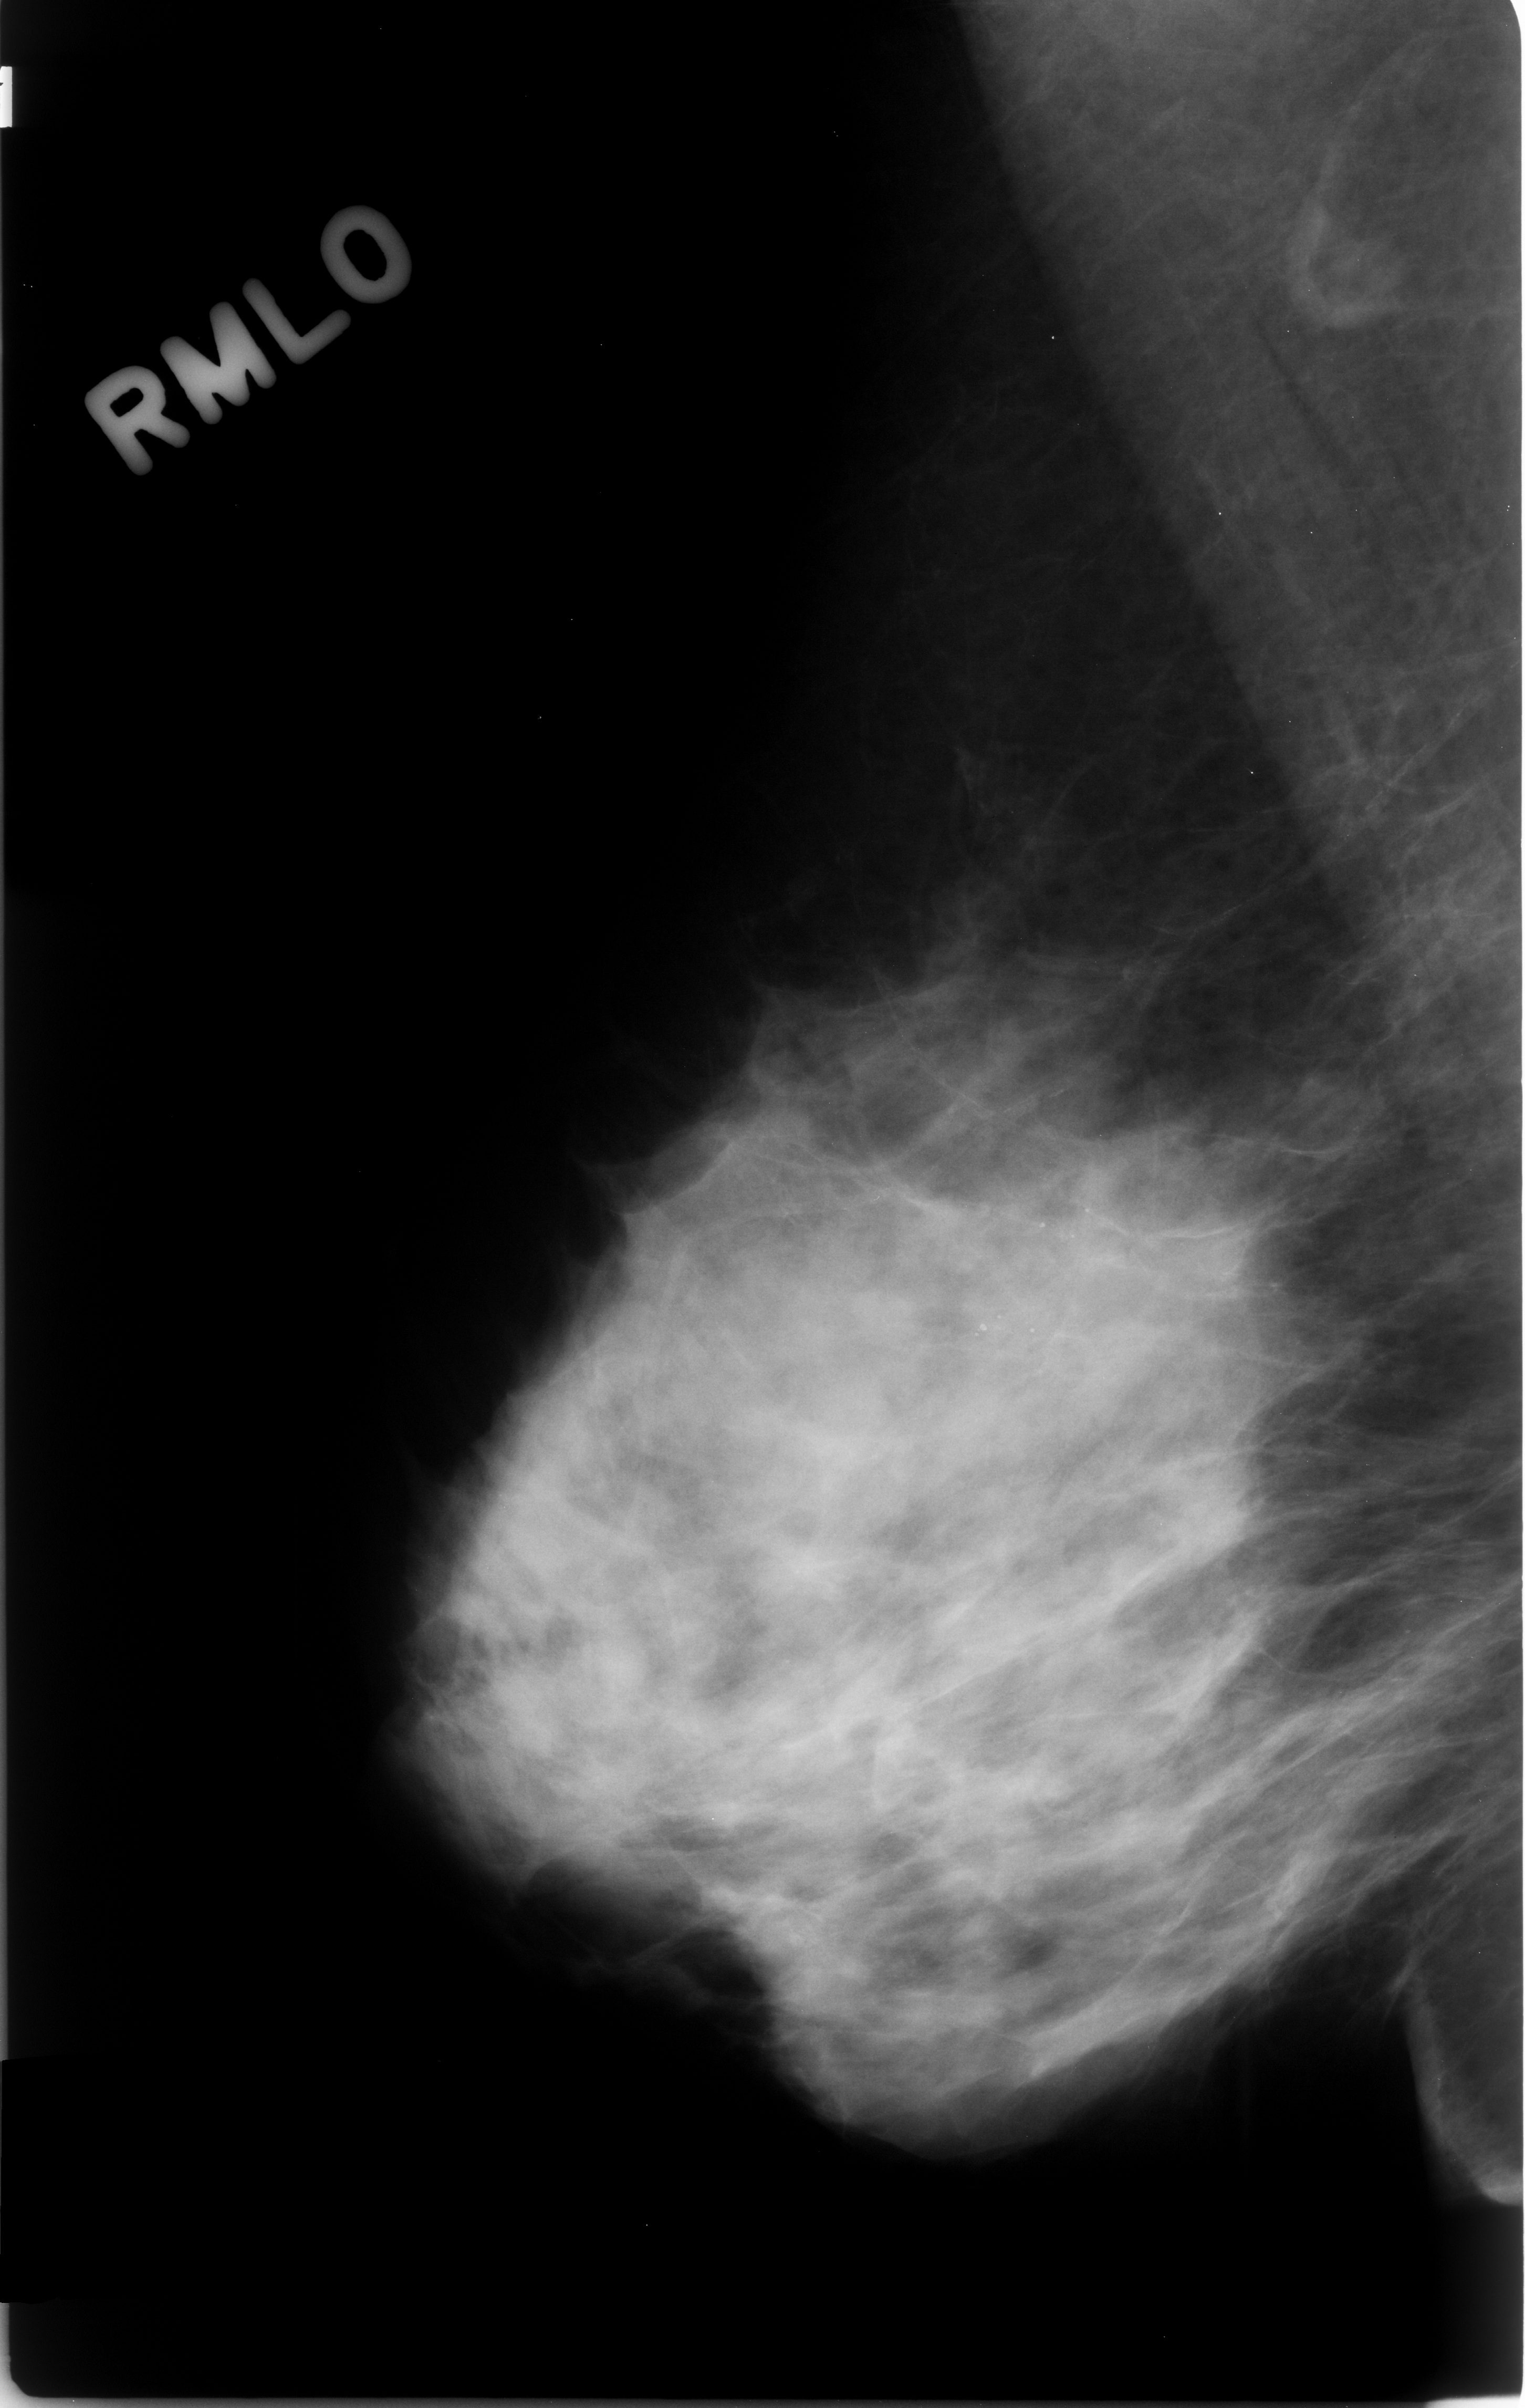
Scanned film-screen mammogram; right breast; MLO view; breast composition: heterogeneously dense (BI-RADS density category 3 of 4); 1525 × 2408 image matrix.
Expert-marked regions of interest on this image (one box per marked abnormality):
- calcifications, morphology round and regular, distribution clustered; BI-RADS assessment category 4; subtlety rating 4 on a 1 (subtle) to 5 (obvious) scale; pathology result (as recorded, not read from the image): benign: bounding box [x1, y1, x2, y2] px = [903, 1138, 1177, 1447]